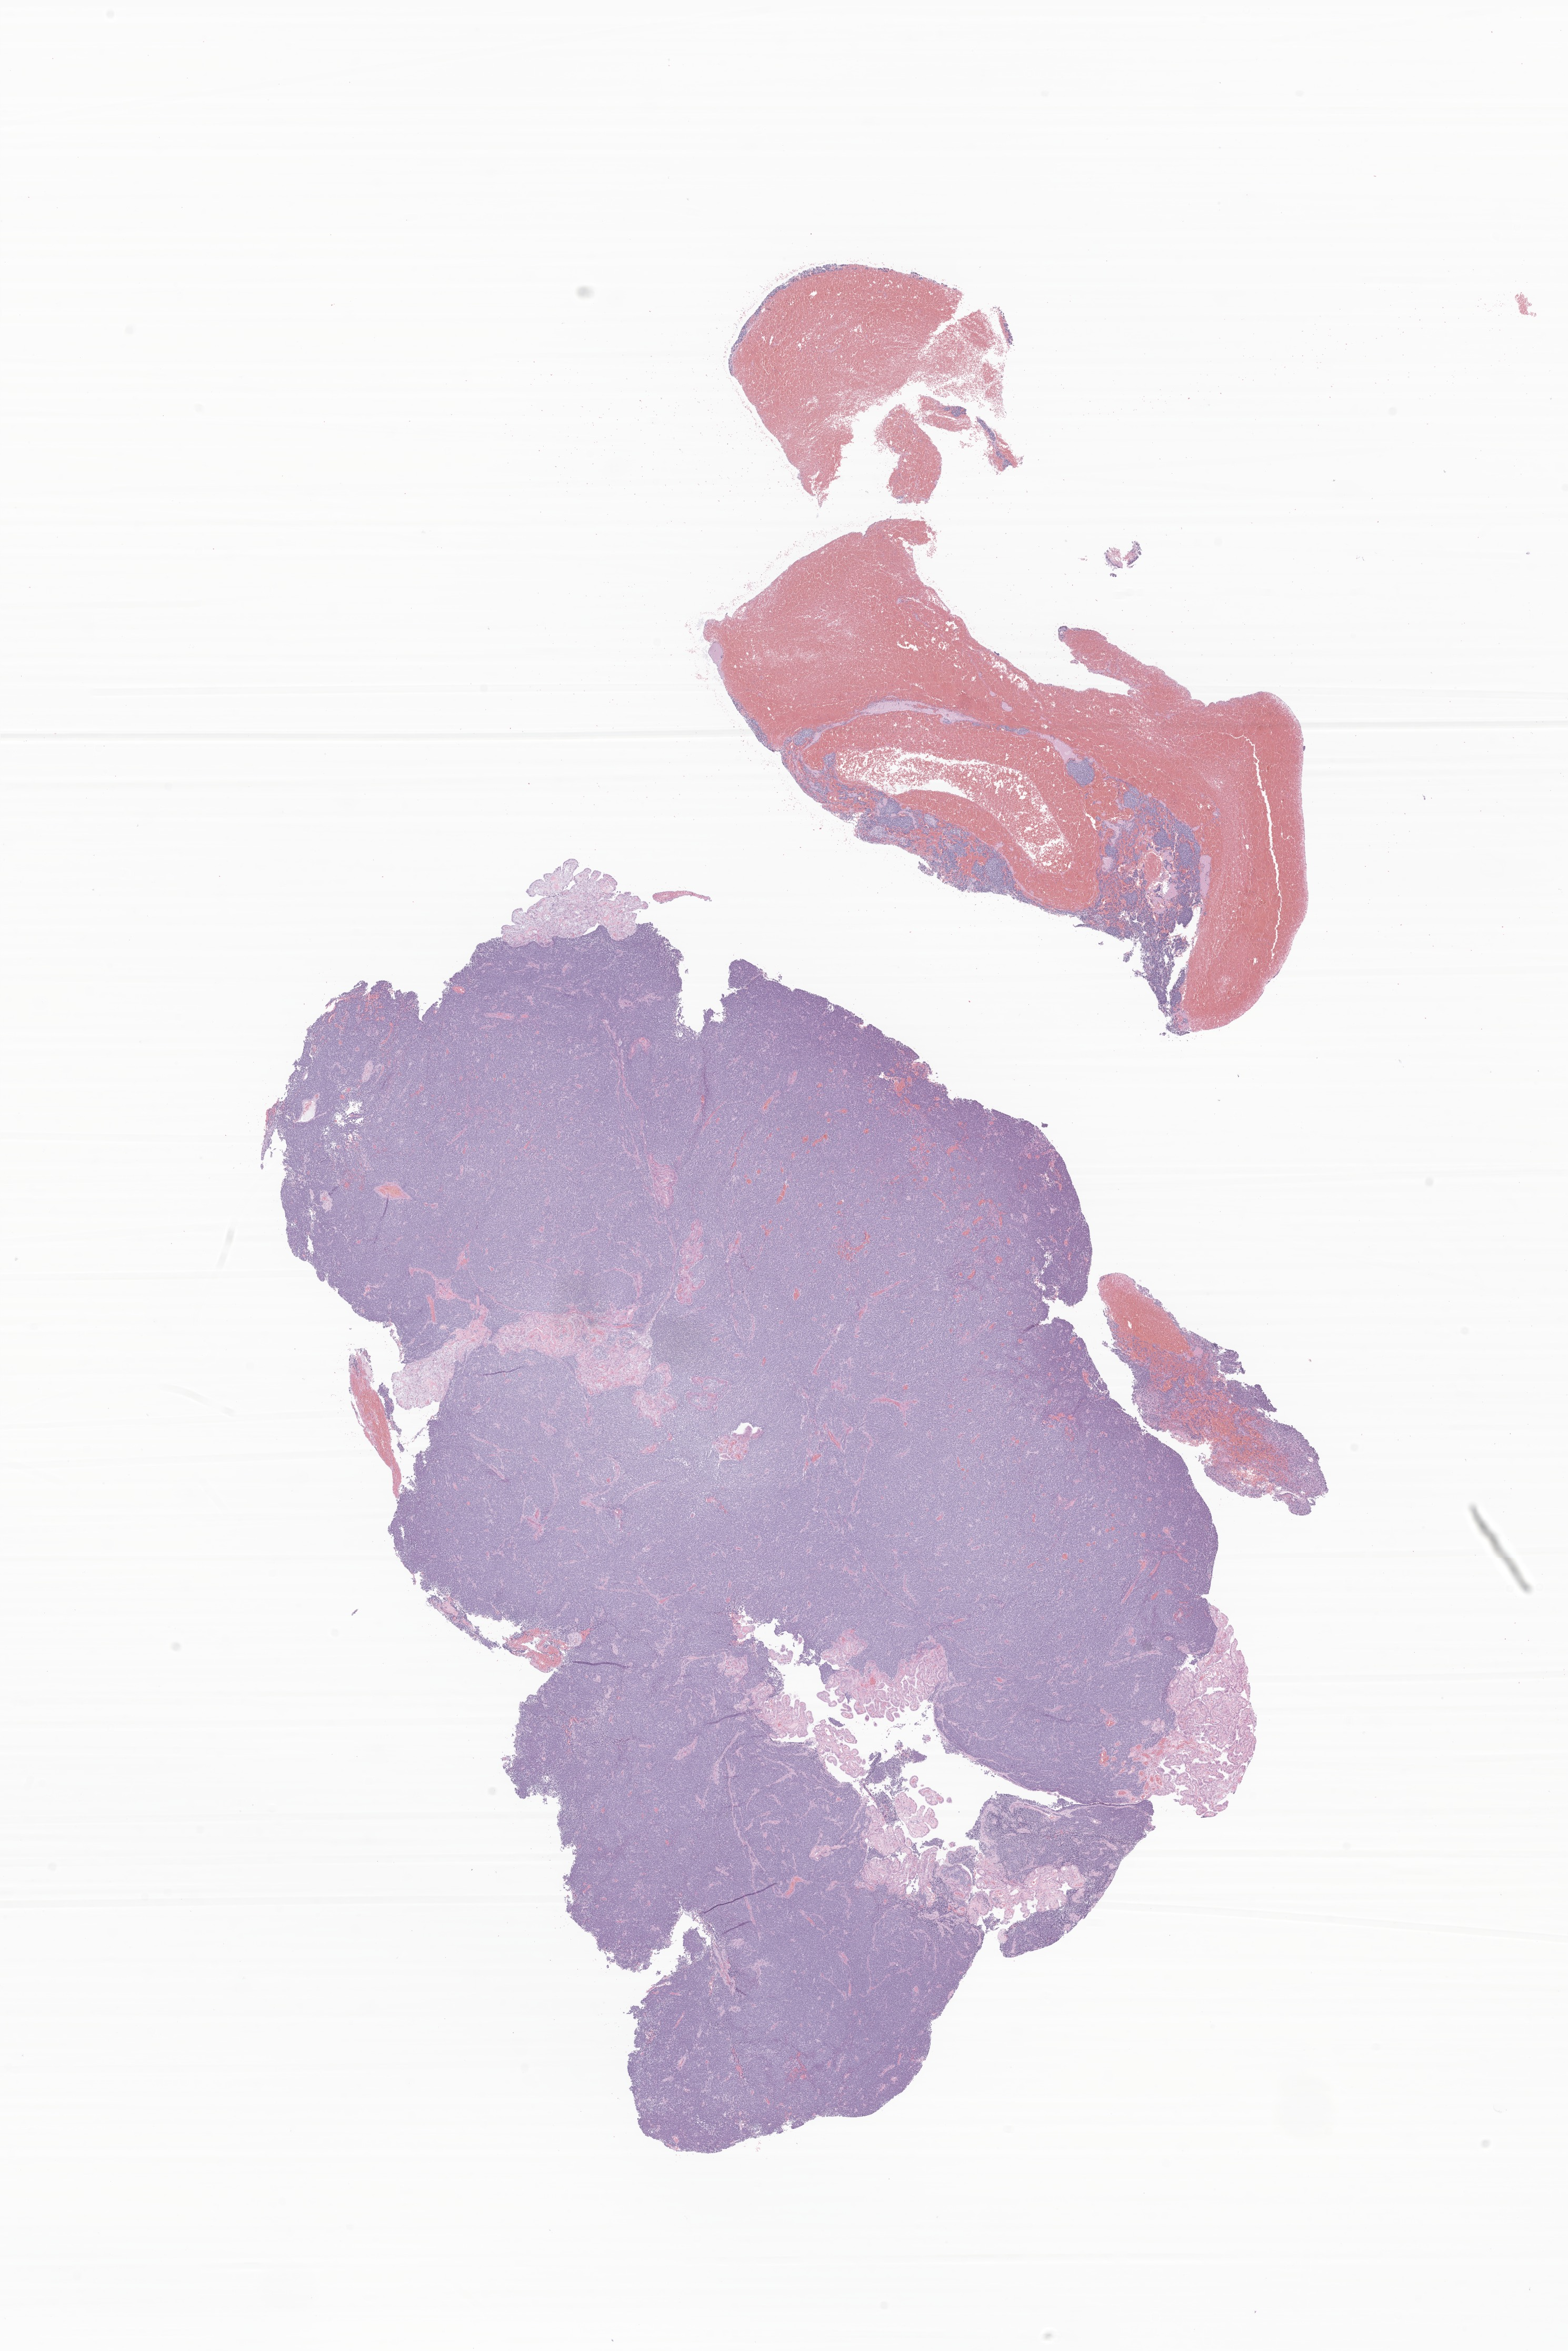
Whole-slide image, haematoxylin and eosin stain of tumor tissue from the brain — a low-resolution overview of the entire scanned area, about 12.6 x 18.8 mm. FFPE section. Patient: female, age 134 months (11 years 2 months).
Diagnosis (ICD-O-3 morphology term): Medulloblastoma, NOS.